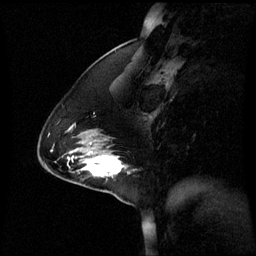
Breast MRI (dynamic contrast-enhanced), one sagittal slice; slice 20 of 60 in the series (ordered by position); dynamic contrast-enhanced series, image 2 of 3 at this slice position (ordered by acquisition); 1.5 T; TE 4.2 ms, TR 8.9 ms; 2.2 mm slice thickness; 256 × 256 image matrix, field of view 240 × 240 mm. Female patient, age 44 years. Case-level facts recorded for this patient, not image findings: setting: breast cancer imaged before/during neoadjuvant chemotherapy; receptor status: triple-negative.
Annotated regions visible in this slice (semi-automatic segmentation, software-assisted and operator-edited):
- analysis volume of interest (the breast-tissue region the enhancement analysis was run in; not a lesion): bounding box <76,150,129,185> (left, top, right, bottom; pixels)
- tumour enhancement mask (voxels above the 70 % enhancement threshold inside the analysis volume of interest): <83,156,123,177>